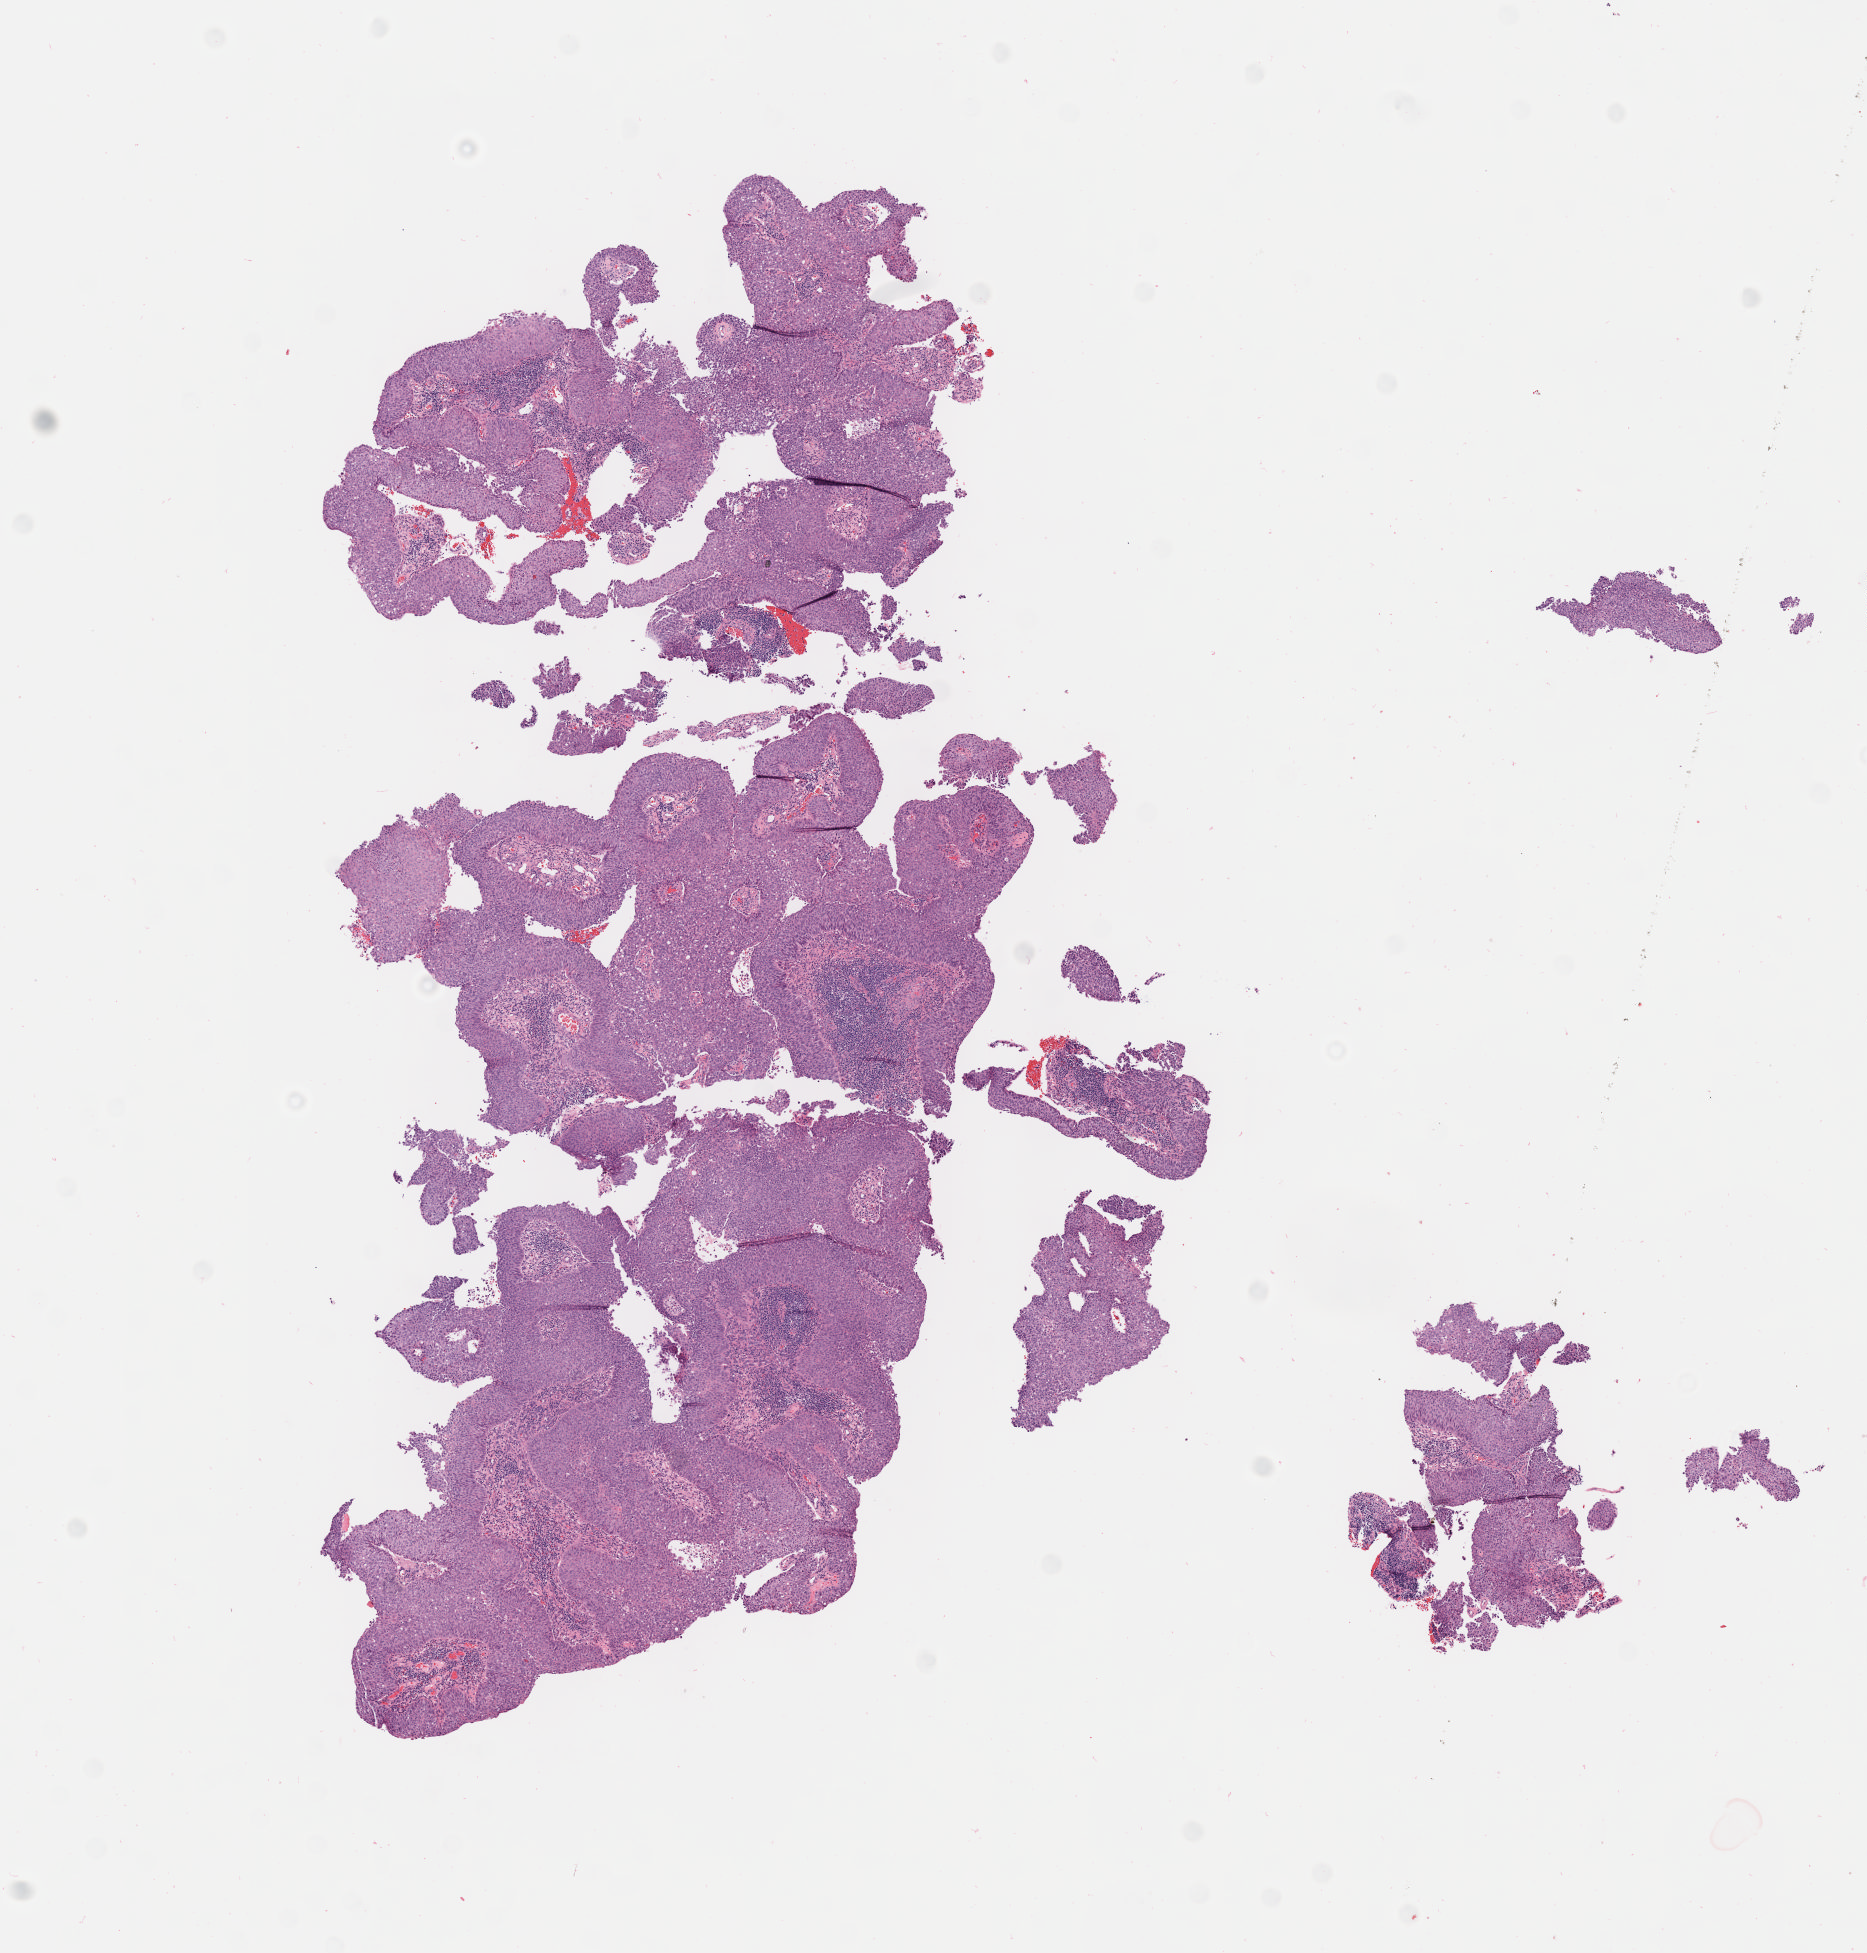
Whole-slide image, hematoxylin and eosin (H&E) stain — low-resolution overview of the scanned area, about 7.6 x 7.9 mm. Tumor tissue. Site: cervix. Female patient, age 42 years.
Histologic diagnosis: Squamous cell carcinoma, large cell, nonkeratinizing, NOS.